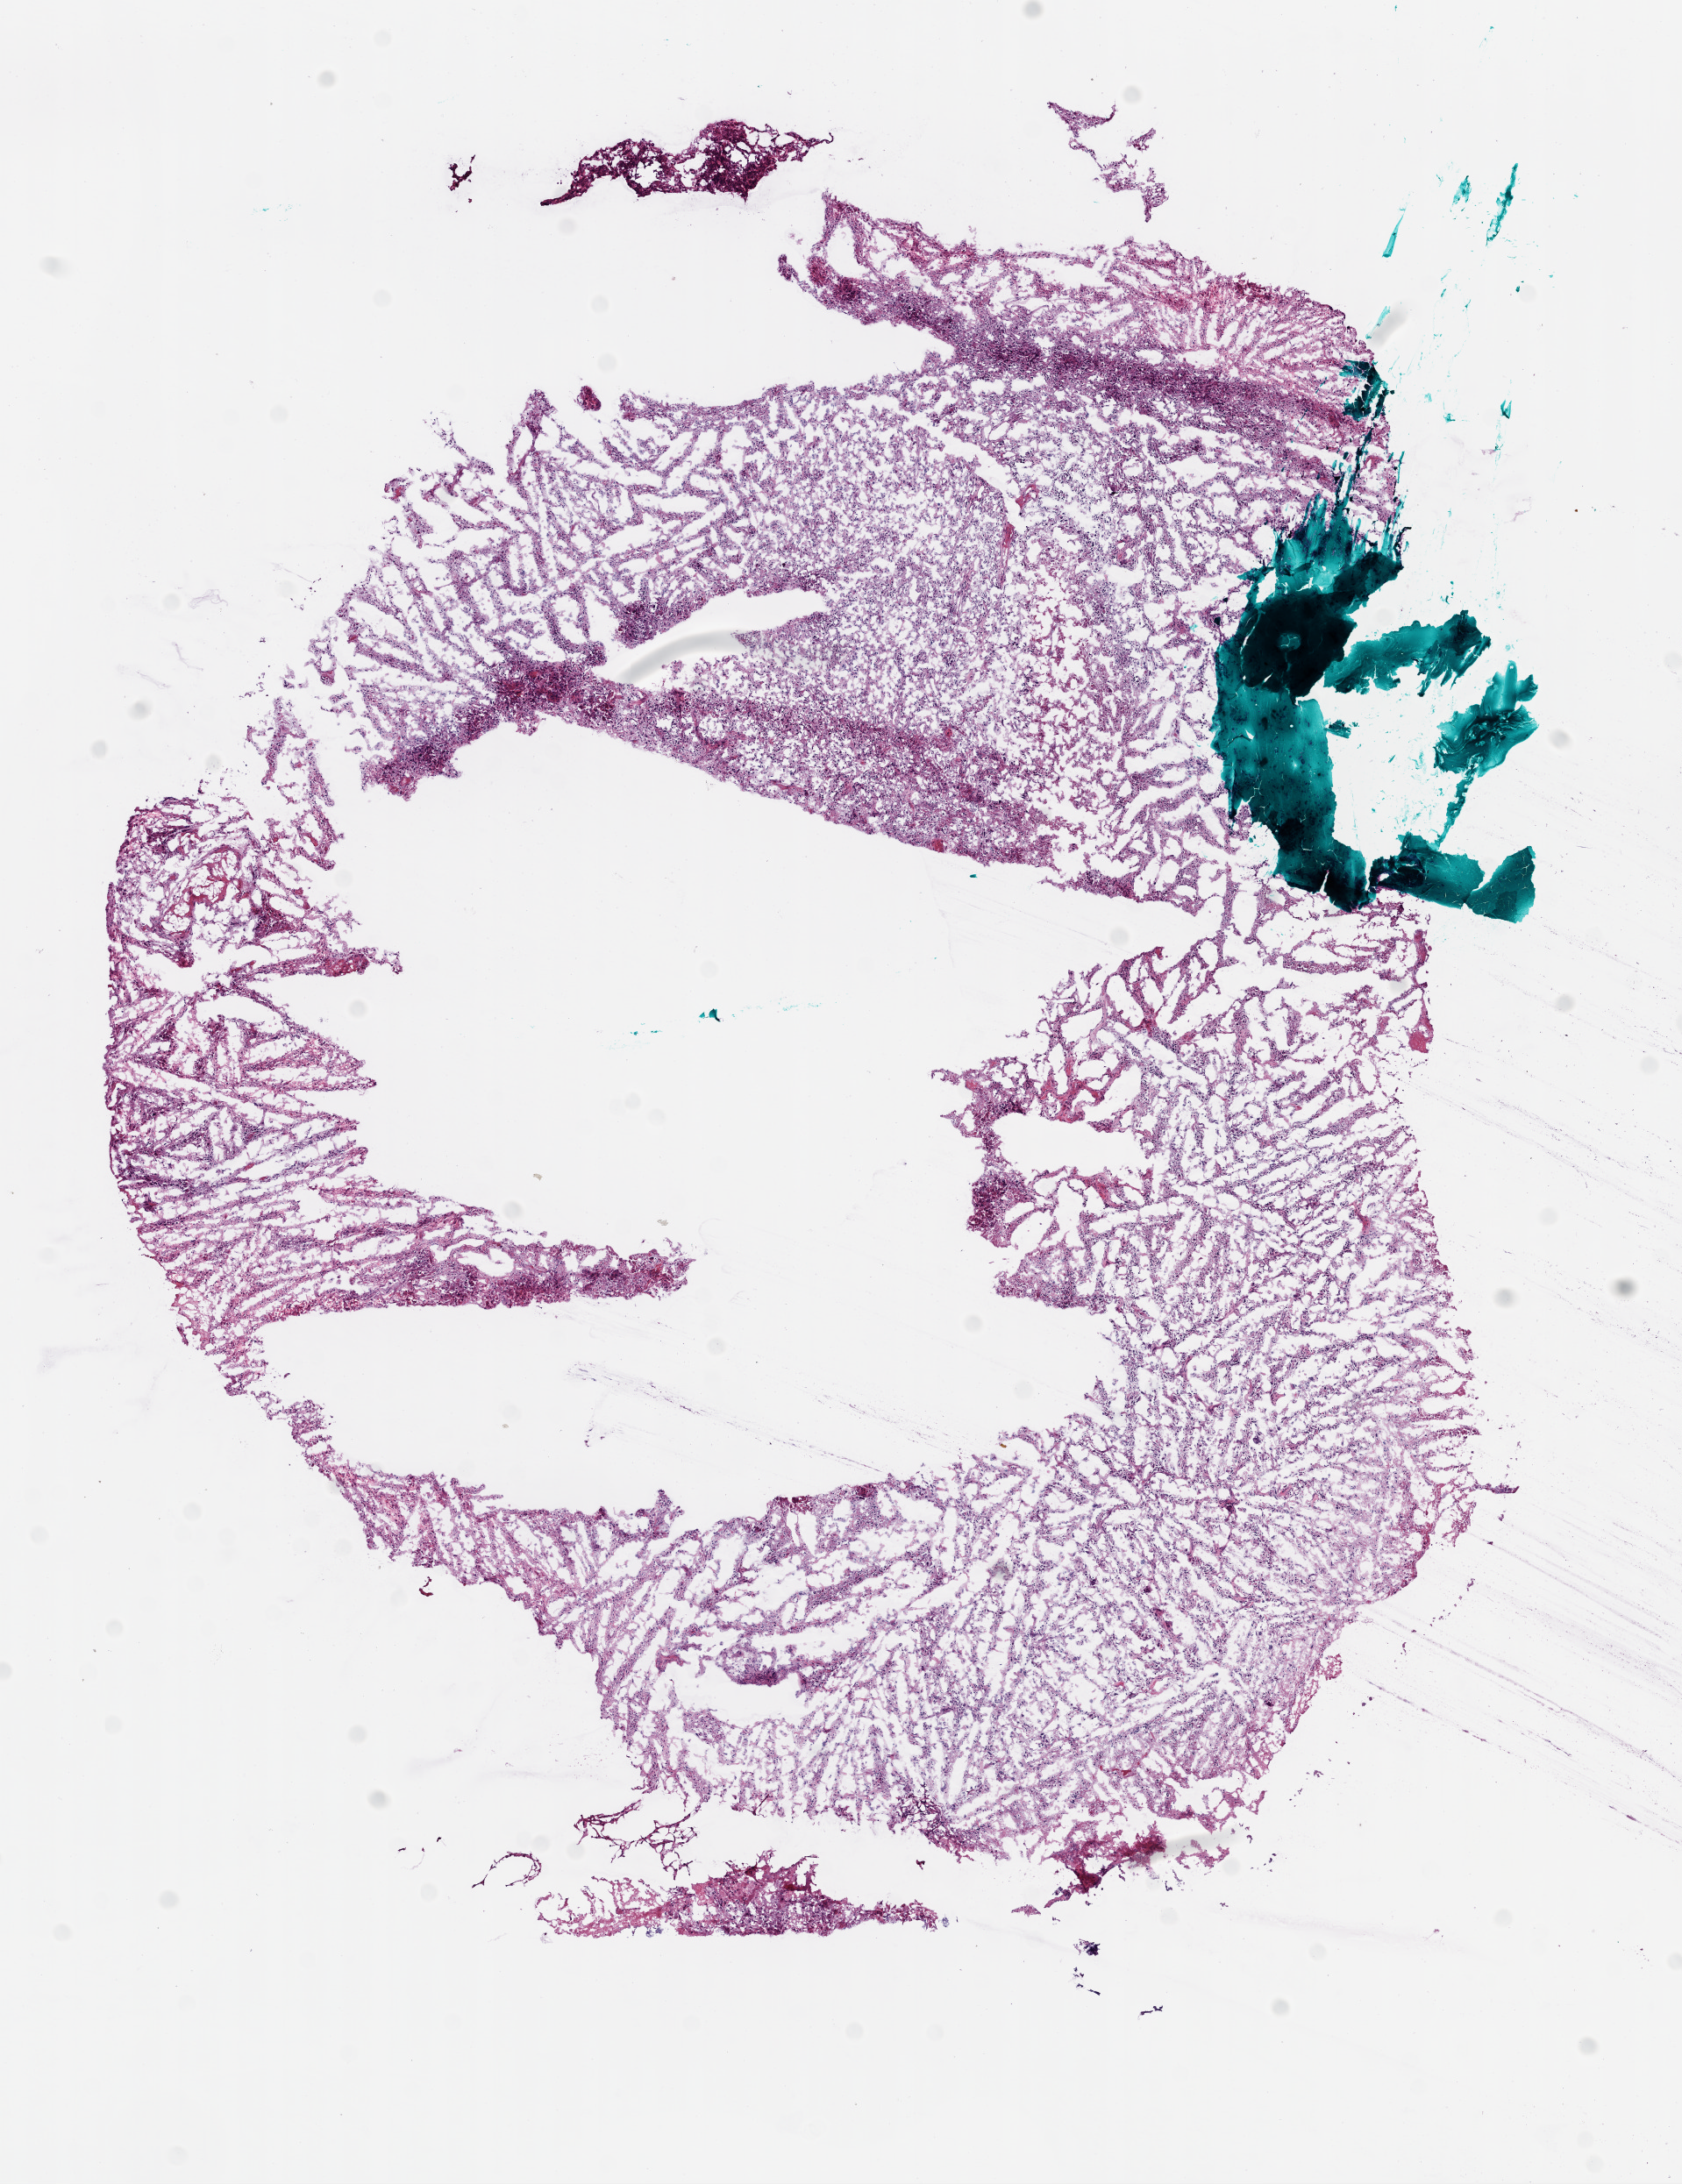
Whole-slide histology image, H&E — low-resolution overview of the scanned area, about 7.7 x 10.0 mm (from a 20x scan), frozen section, brain, primary tumour sample. Female patient; age at initial diagnosis 53 years. Pathologist review of this section (percent, as recorded): tumour cells 85%, tumour nuclei 90%, normal cells 10%, stromal cells 5%, necrosis 0%.
Pathologic diagnosis: Glioblastoma.